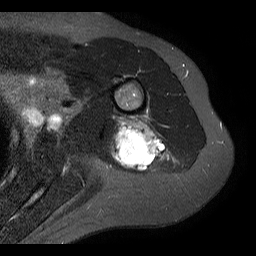
MRI of an extremity soft-tissue mass, one axial slice; position 7 of 20 along the scan axis; STIR; 4 mm slice thickness; 256 × 256 image matrix. Female patient. Case-level facts recorded for this patient, not image findings: histological type: malignant fibrous histiocytoma; grade: low; site of the primary tumour: left arm.
Outlined on this slice (outlined manually by an expert reader):
- gross tumour volume (mass): bounding box (x1, y1, x2, y2) in pixels: (111, 121, 170, 172)